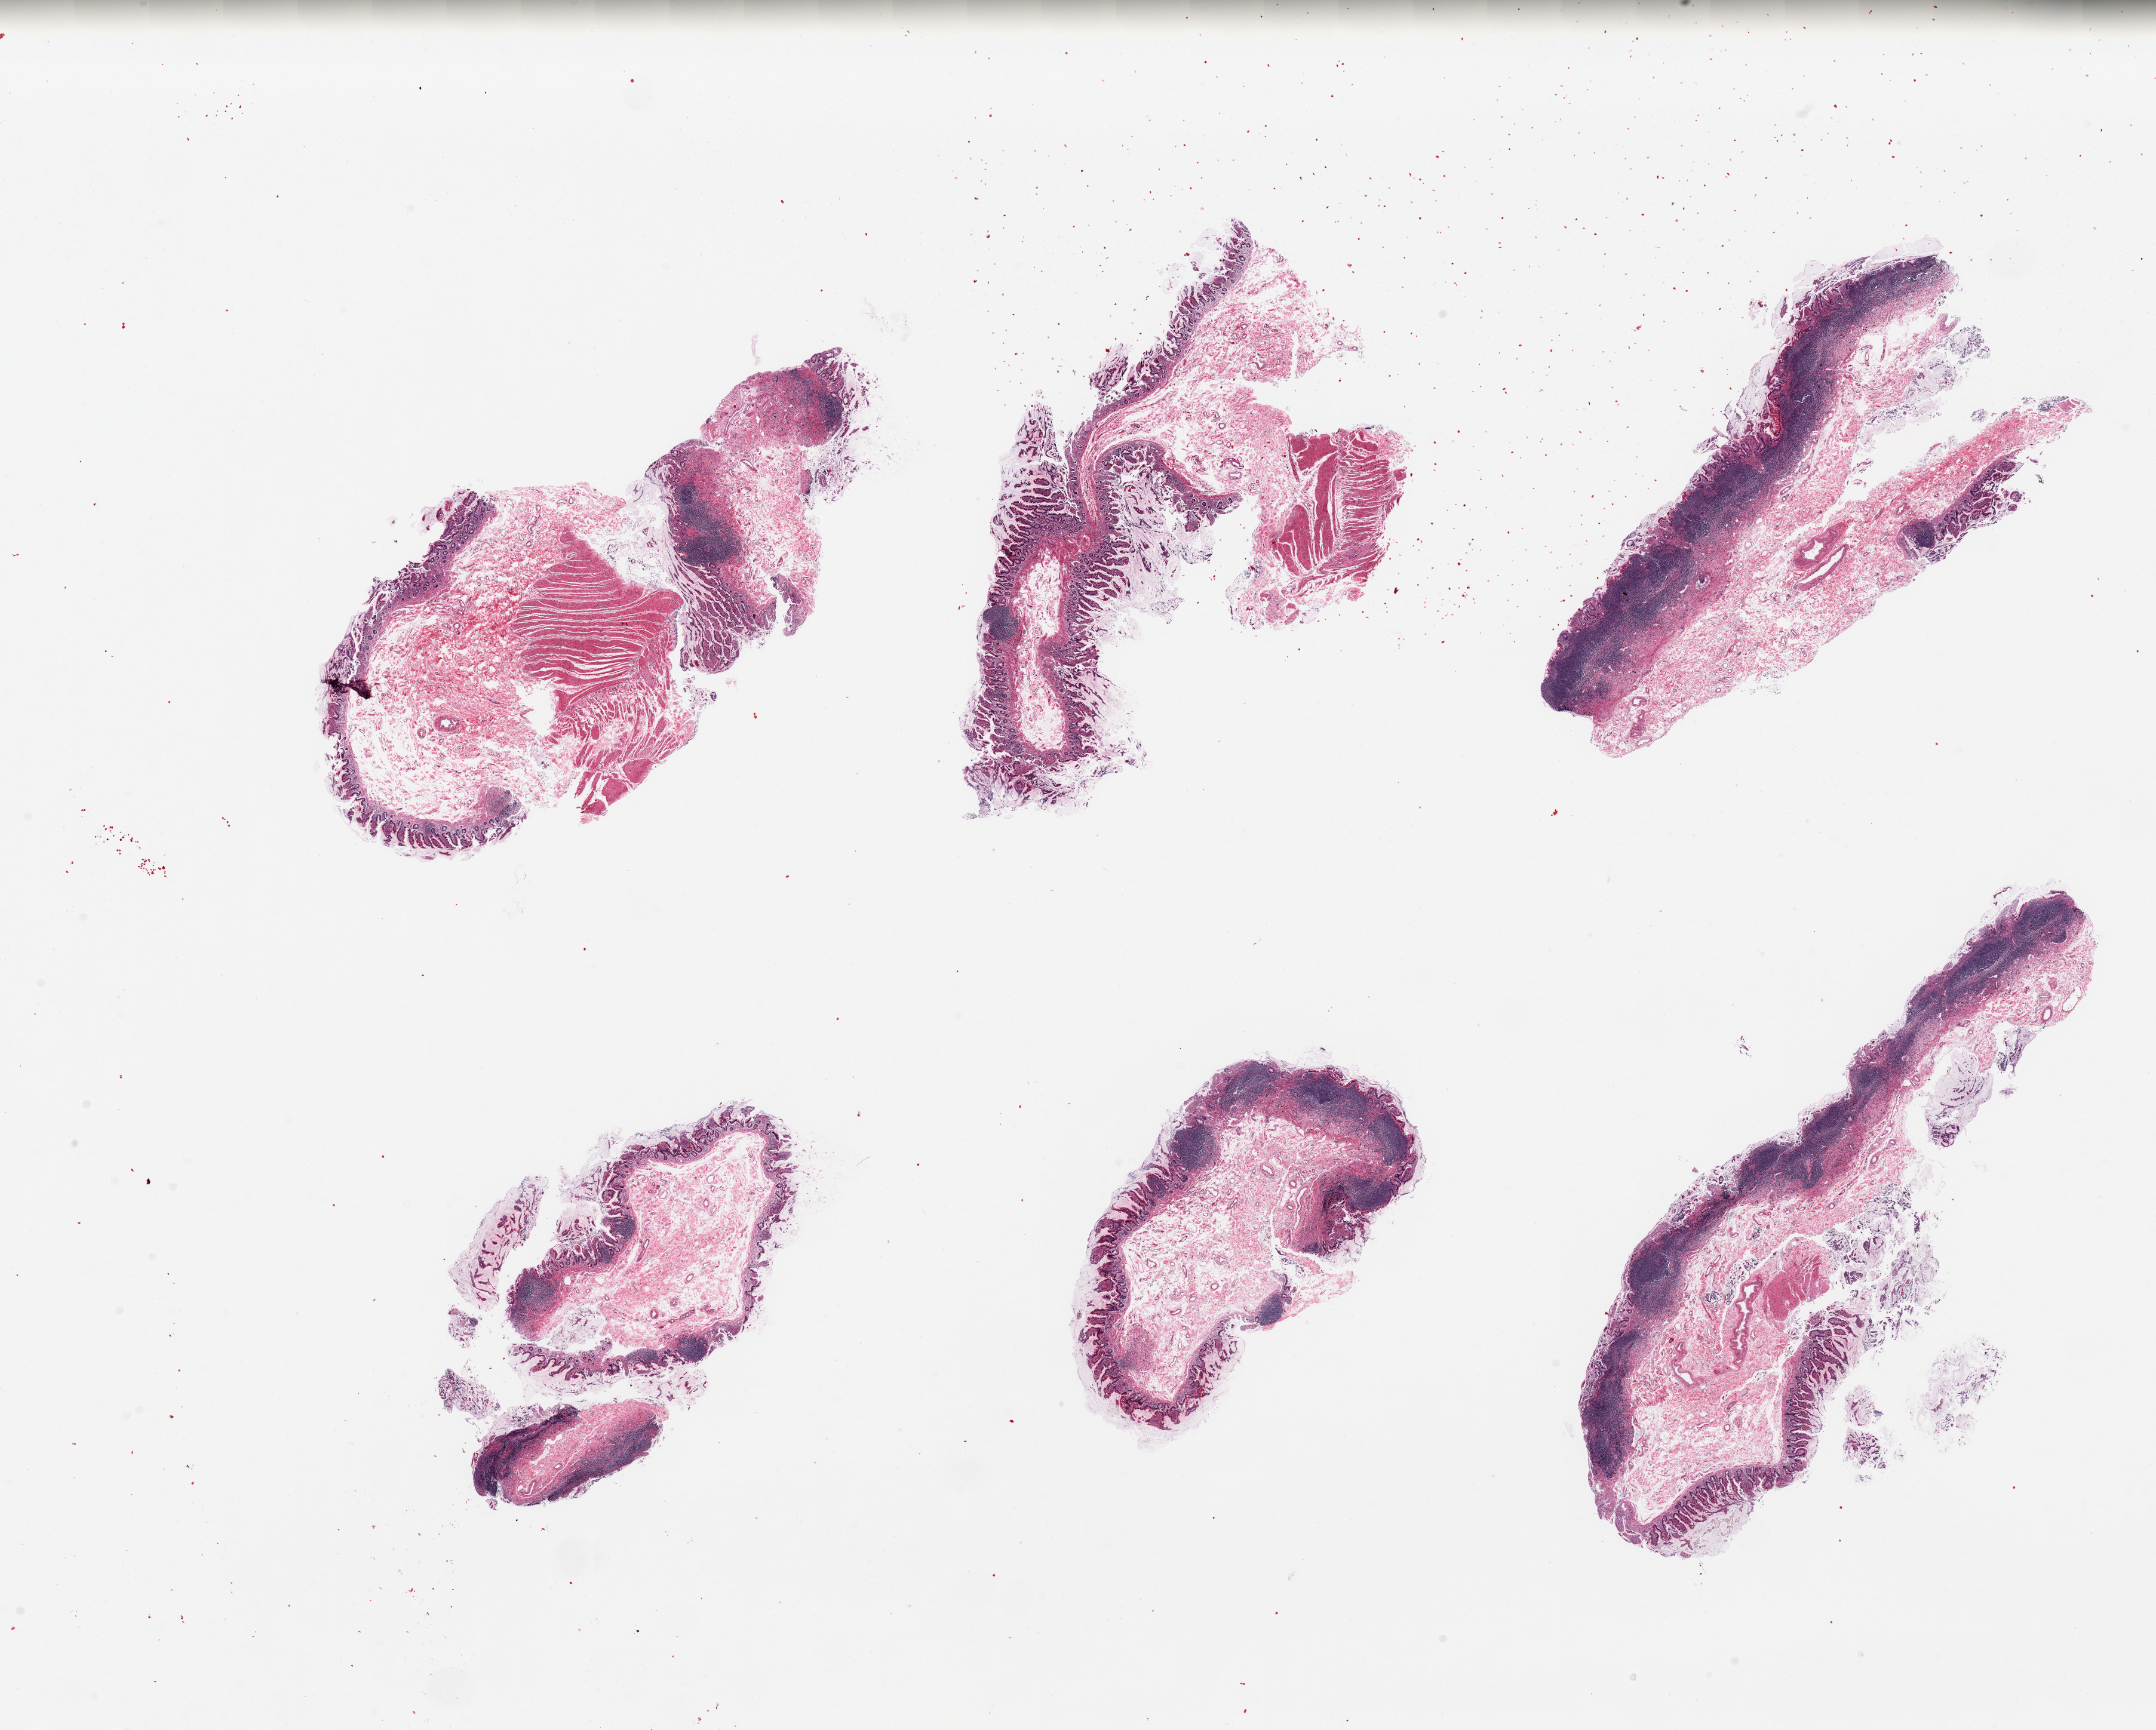
Digitized H&E-stained section — shown as a low-resolution overview of the whole scanned area (about 28.5 x 22.9 mm, slide scanned at 20x), PAXgene-fixed paraffin-embedded (PFPE) section, target tissue: ileum, tissue donor sample. Female donor.
Reviewer comment on this tissue sample: 6 pieces; abundant lymphoid tissue.